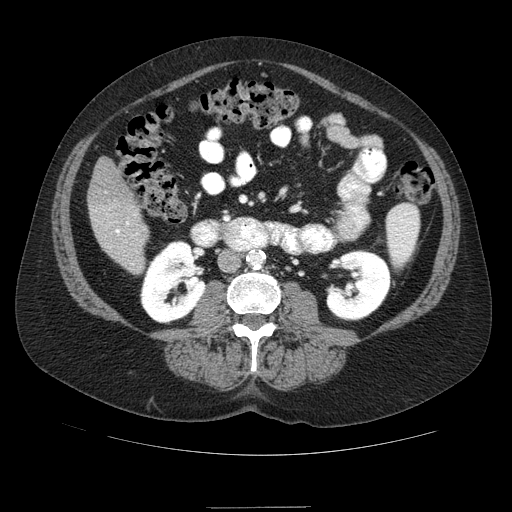
Contrast-enhanced abdominal CT (liver protocol), one axial slice. Slice 20 of 89 in the series (ordered by position). 120 kVp. Soft-tissue window (W 400 / L 40 HU). 2.5 mm slice thickness. 512 × 512 image matrix. From the clinical record (not read from this slice): diagnosis: hepatocellular carcinoma (patient treated with transarterial chemoembolisation; whether this scan precedes or follows treatment is not stated here); TNM stage (as recorded): Stage-IIIB.
Structures marked on this image (semi-automatically segmented with operator editing):
- liver parenchyma outside the tumour (the mass and vessels are separate outlines, so this box may not span the whole liver): box from (x=88, y=156) to (x=148, y=272) px
- liver vessels: (x=116, y=222)–(x=129, y=234)